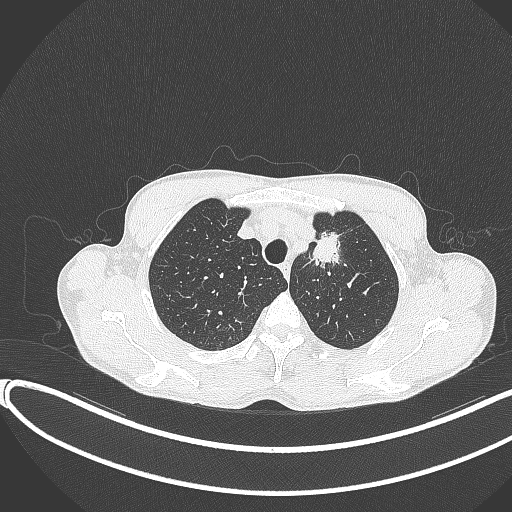
Chest CT, one axial slice. Slice 317 of 374 in the series (ordered by position). 120 kVp. Lung window (W 1500 / L -600 HU). 1 mm slice thickness. 512 × 512 image matrix. Male patient, age 58 years. Case-level facts recorded for this patient, not image findings: clinical TNM (as recorded): T1c N1 M0.
Outlined on this slice (rectangle marked by the reading radiologist):
- lung tumour (recorded histology: adenocarcinoma): bounding box (x1, y1, x2, y2) in pixels: (307, 227, 358, 275)